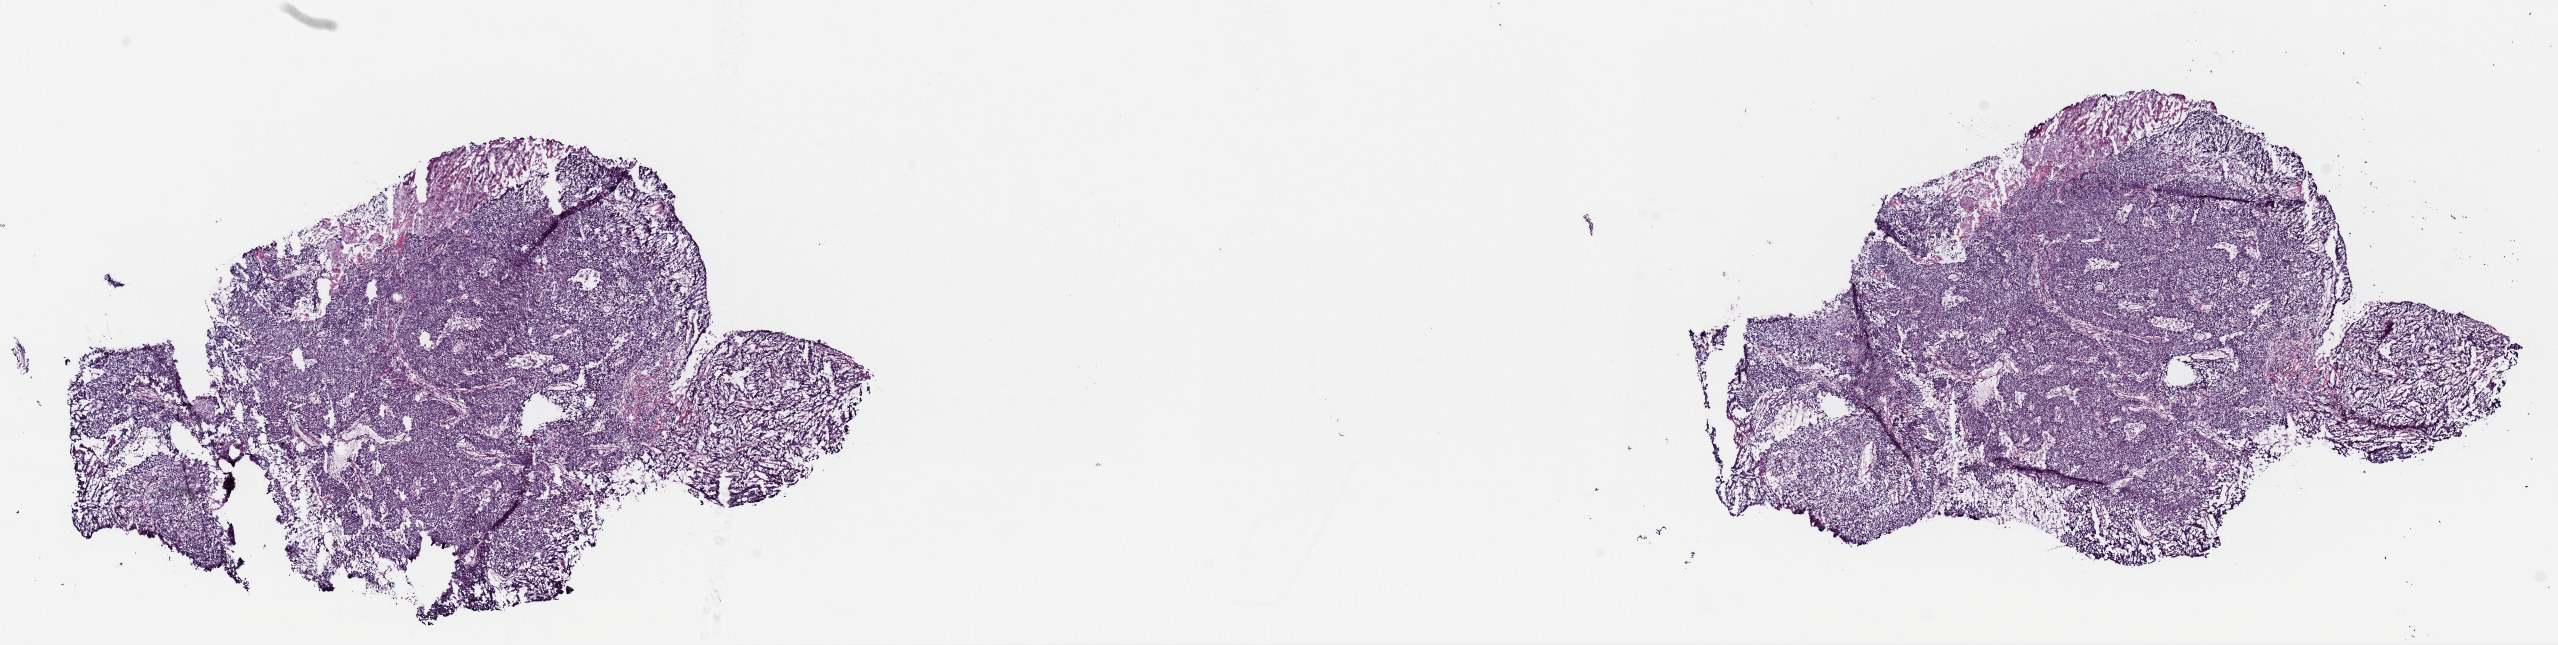
Digitized H&E-stained tissue section (whole slide) — a low-resolution overview of the entire scanned area, about 20.2 x 5.1 mm (acquisition: 40x scan), frozen section, uterus, primary tumour sample. Female, age 60 years at initial diagnosis. Histologic grade: G3 (poorly differentiated). Slide review estimates, as recorded: tumour cells 80%, tumour nuclei 80%, normal cells 0%, stromal cells 10%, necrosis 10%. Infiltration values recorded for this section: lymphocyte infiltration 40%, monocyte infiltration 40%, neutrophil infiltration 10%.
* histologic diagnosis: Endometrioid adenocarcinoma, NOS (endometrium)
* FIGO stage: IB